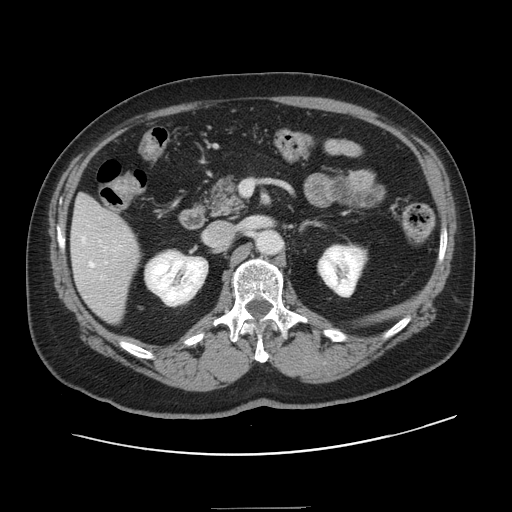
Contrast-enhanced abdominal CT, one axial slice; slice 65 of 143 in the series (ordered by position); soft-tissue window (W 400 / L 40 HU); 512 × 512 image matrix. Male patient, age 62 years. Case-level facts recorded for this patient, not image findings: diagnosis: colorectal cancer liver metastases, imaged before liver resection; multiple liver metastases: yes; largest metastasis: 2.7 cm; disease in both lobes: no.
Outlined on this slice (outlined manually by an expert reader):
- hepatic veins: box from (x=82, y=237) to (x=94, y=267) px
- liver: (x=72, y=196)–(x=139, y=323)
- planned liver remnant (the part of the liver to remain after resection): (x=77, y=196)–(x=98, y=212)
- portal vein (with intrahepatic branches): (x=99, y=241)–(x=115, y=263)